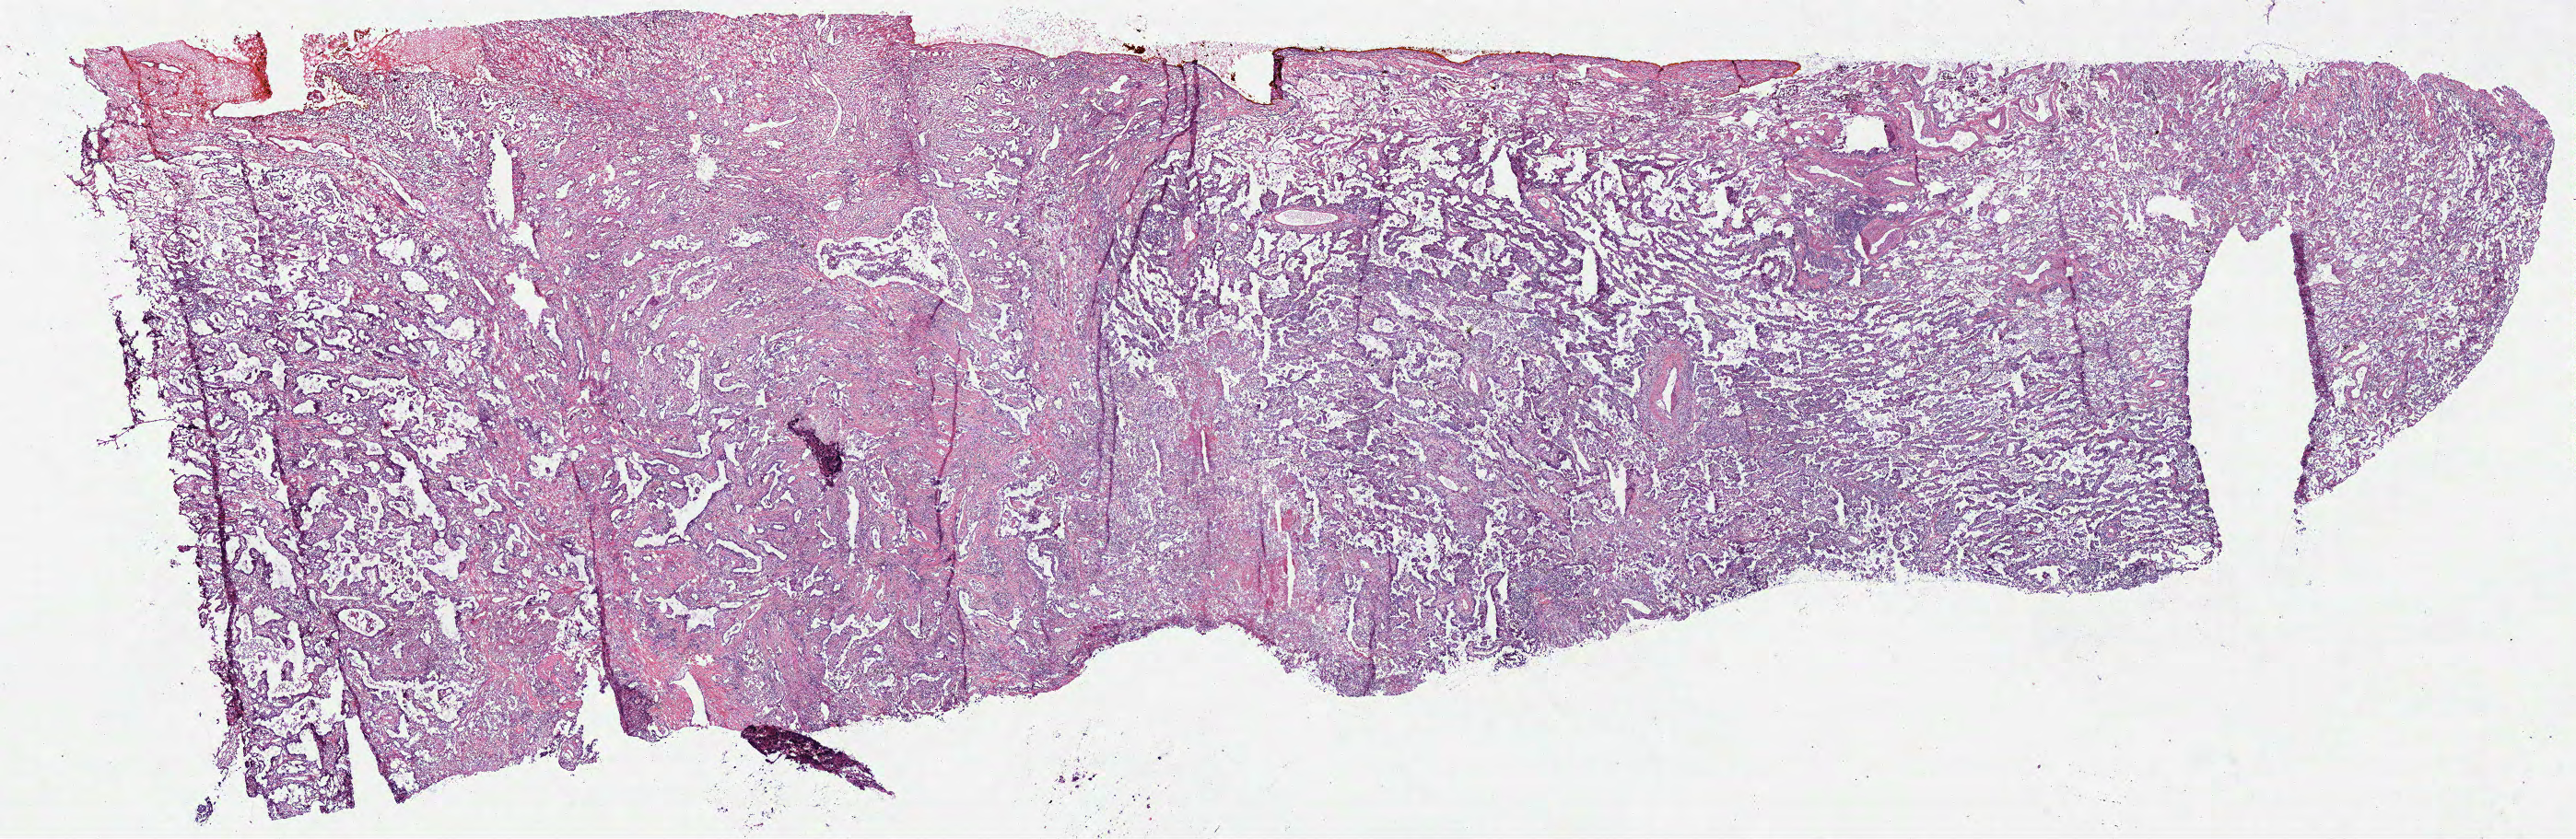
Whole-slide histology image, H&E-stained — shown as a low-resolution overview of the whole scanned area (about 22.0 x 7.2 mm, slide scanned at 40x). Frozen section from the bottom of the tissue portion. Sample: primary tumour, lung. Patient: female, age at initial diagnosis 64 years.
Pathologic diagnosis: Adenocarcinoma with mixed subtypes (upper lobe, lung).